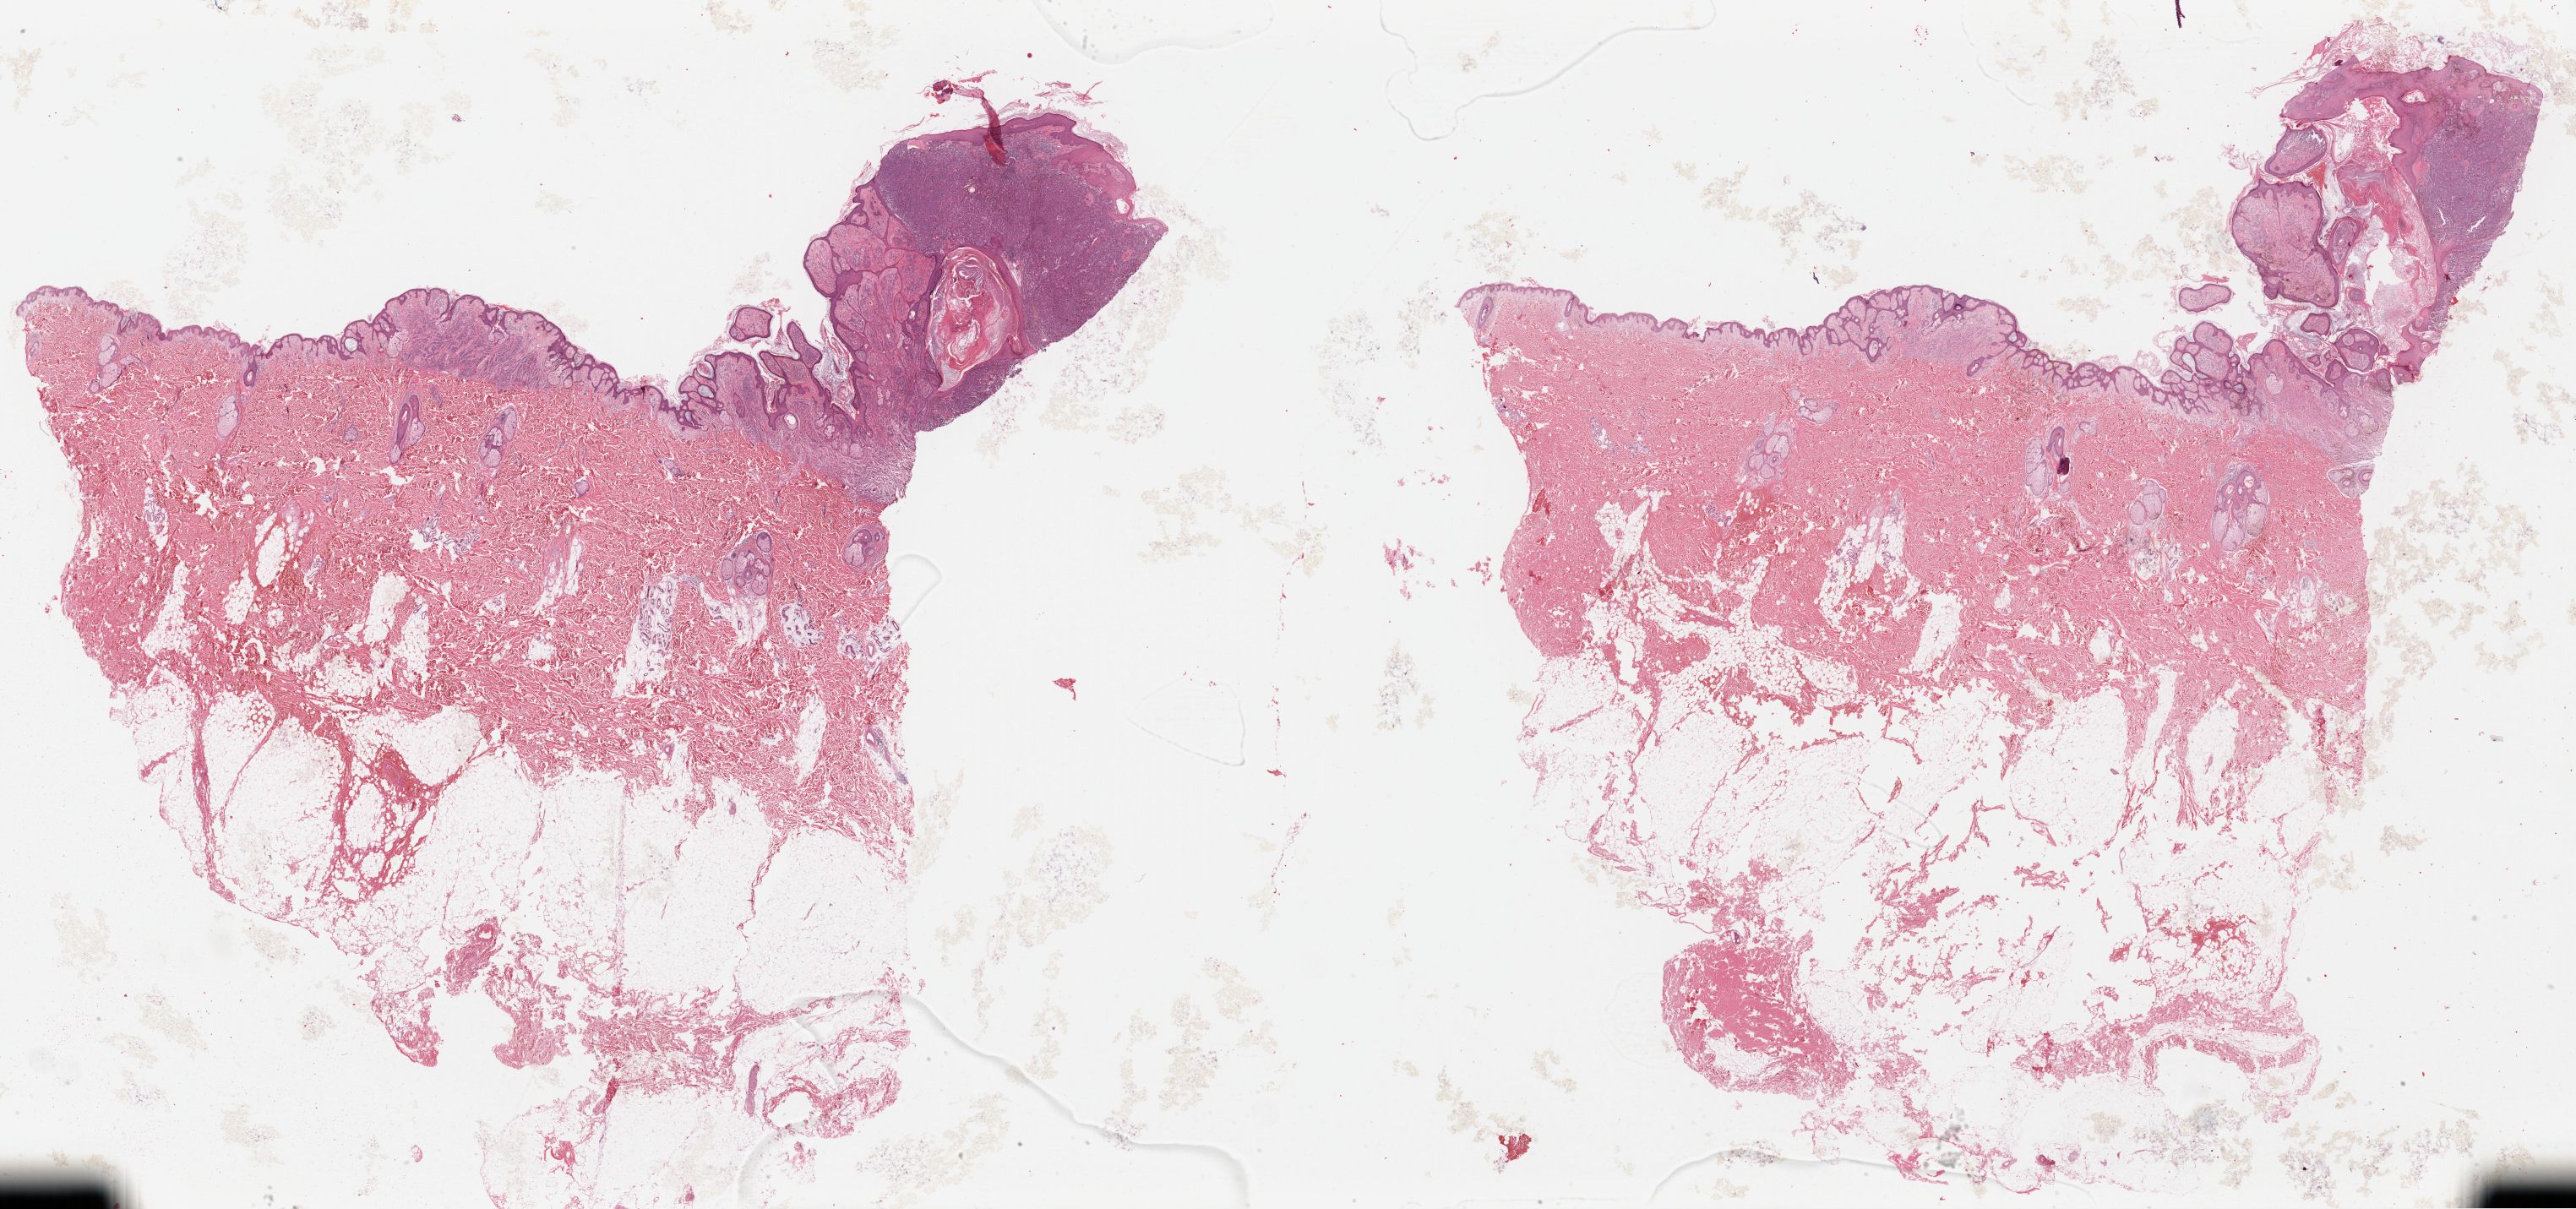
Whole-slide histology image, Hematoxylin and eosin (H&E) stained — shown as a low-resolution overview of the whole scanned area (about 47.9 x 22.5 mm, slide scanned at 40x), formalin-fixed paraffin-embedded (FFPE) diagnostic section, skin, primary tumour sample. Male patient; age at initial diagnosis 43 years.
Diagnosis: Malignant melanoma, NOS.